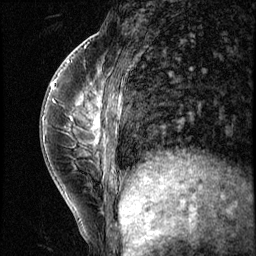
Breast MRI (dynamic contrast-enhanced), one sagittal slice. Position 20 of 56 along the scan axis. 3 images stored at this slice position (order not interpretable as contrast timing). 1.5 T. TE 4.2 ms, TR 8.7 ms. 2.5 mm slice thickness. 256 × 256 image matrix, field of view 180 × 180 mm. Patient: female, 35 years. From the clinical record (not read from this slice): setting: breast cancer imaged before/during neoadjuvant chemotherapy; receptor status: HER2-positive.
Structures marked on this image (semi-automatically segmented with operator editing):
- analysis volume of interest (the breast-tissue region the enhancement analysis was run in; not a lesion): box from (x=58, y=84) to (x=138, y=186) px
- tumour enhancement mask (voxels above the 140 % enhancement threshold inside the analysis volume of interest): (x=92, y=94)–(x=120, y=172)